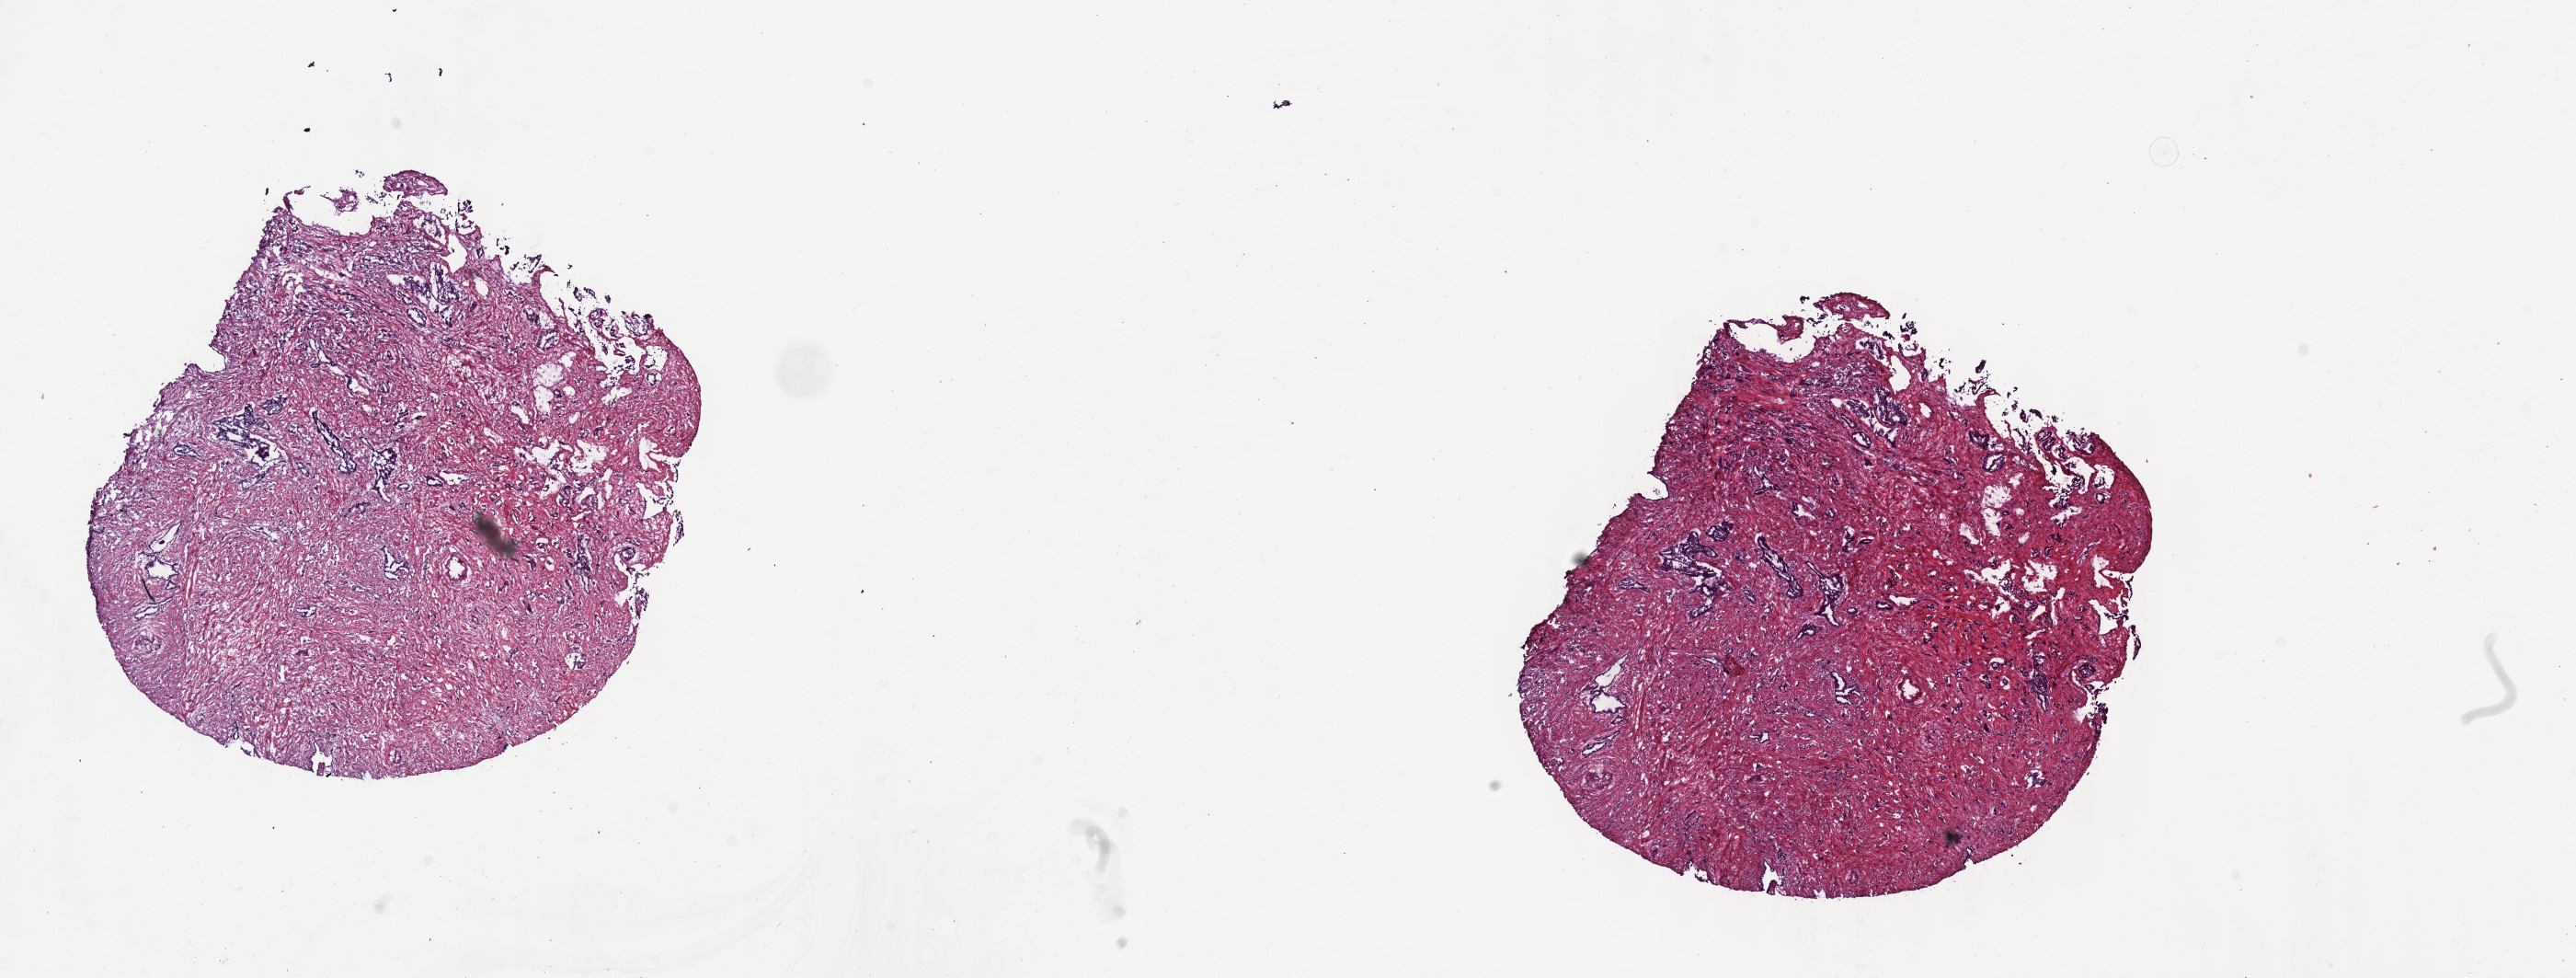
Hematoxylin and eosin (H&E) stained whole-slide image, low-resolution overview of the scanned area, about 22.7 x 8.6 mm; frozen section from the top of the tissue portion; sample: primary tumour, prostate. Patient: male, age at initial diagnosis 66 years. Gleason score: 9 (4+5). Composition of this section per pathologist review: tumour cells 70%, tumour nuclei 70%, normal cells 10%, stromal cells 20%, necrosis 0%. Infiltration values recorded for this section: lymphocyte infiltration 0%, monocyte infiltration 0%, neutrophil infiltration 0%.
Diagnosis: Adenocarcinoma, NOS (prostate gland).